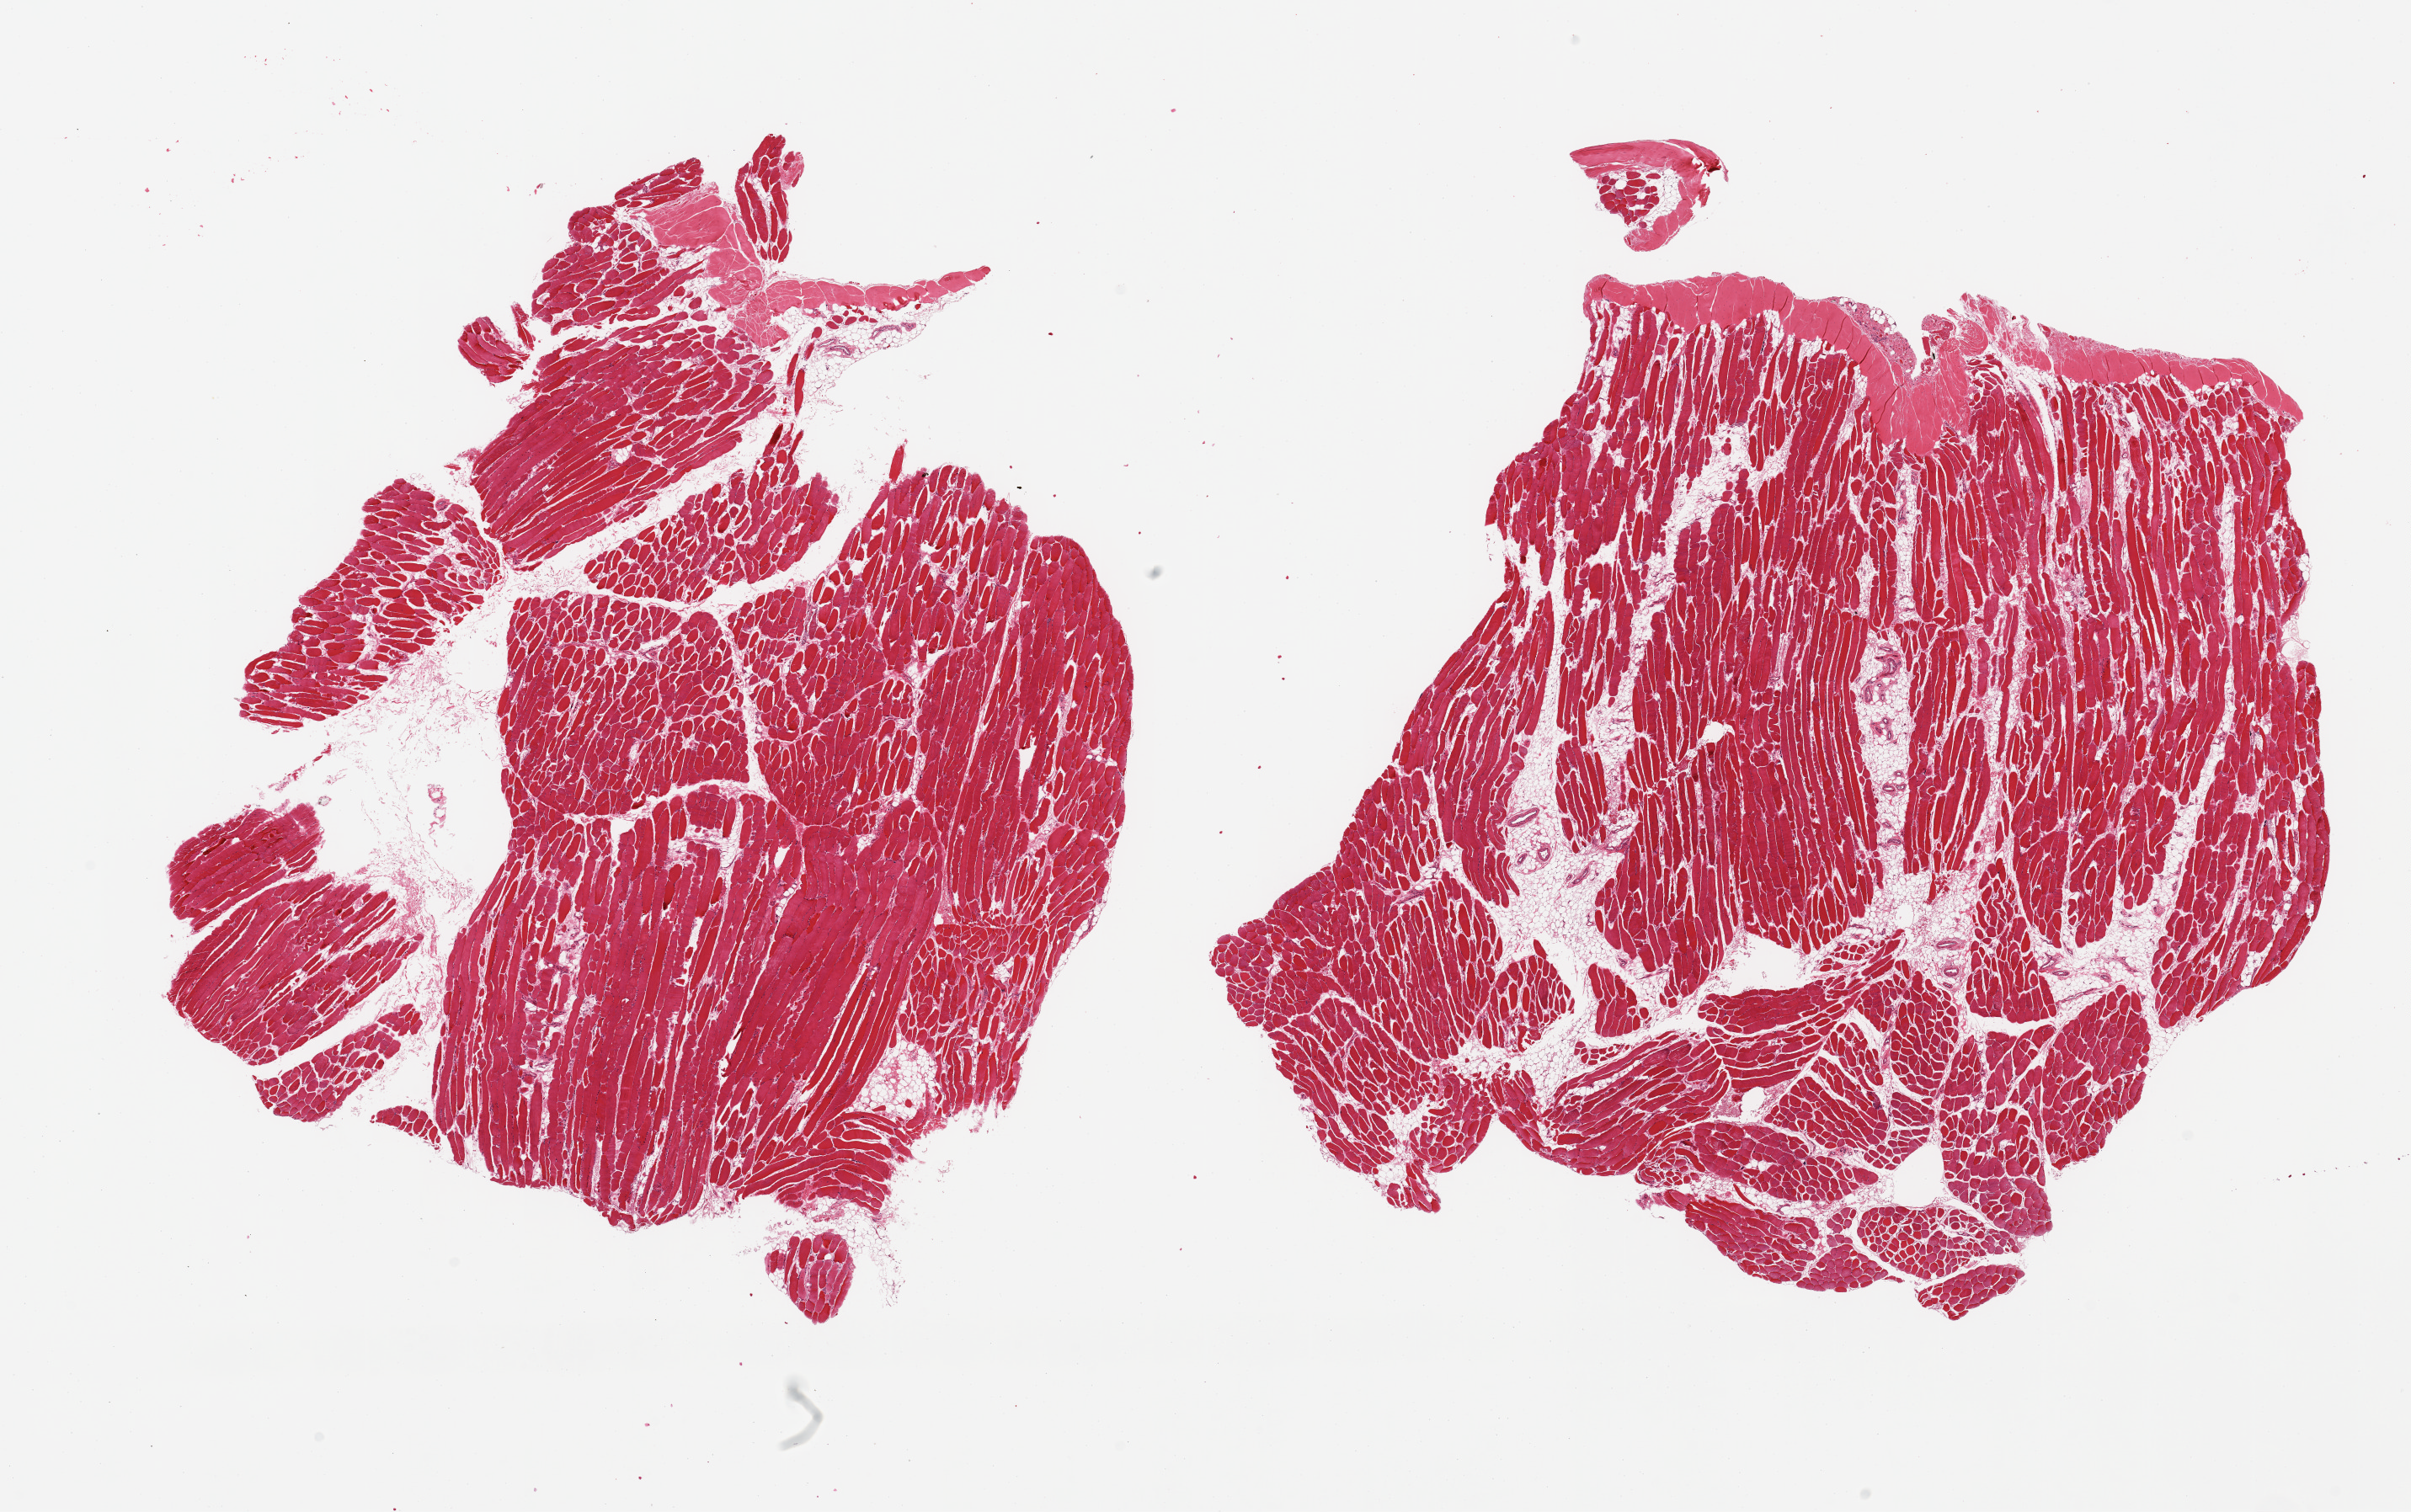
Digitized hematoxylin and eosin (H&E)-stained section — shown as a low-resolution overview of the whole scanned area (about 22.6 x 14.2 mm), PAXgene-fixed paraffin-embedded (PFPE) section, section of skeletal muscle (target tissue), donor tissue sample. Male donor.
Pathologist's review note for this sample: 2 pieces; ~10% internal fat.